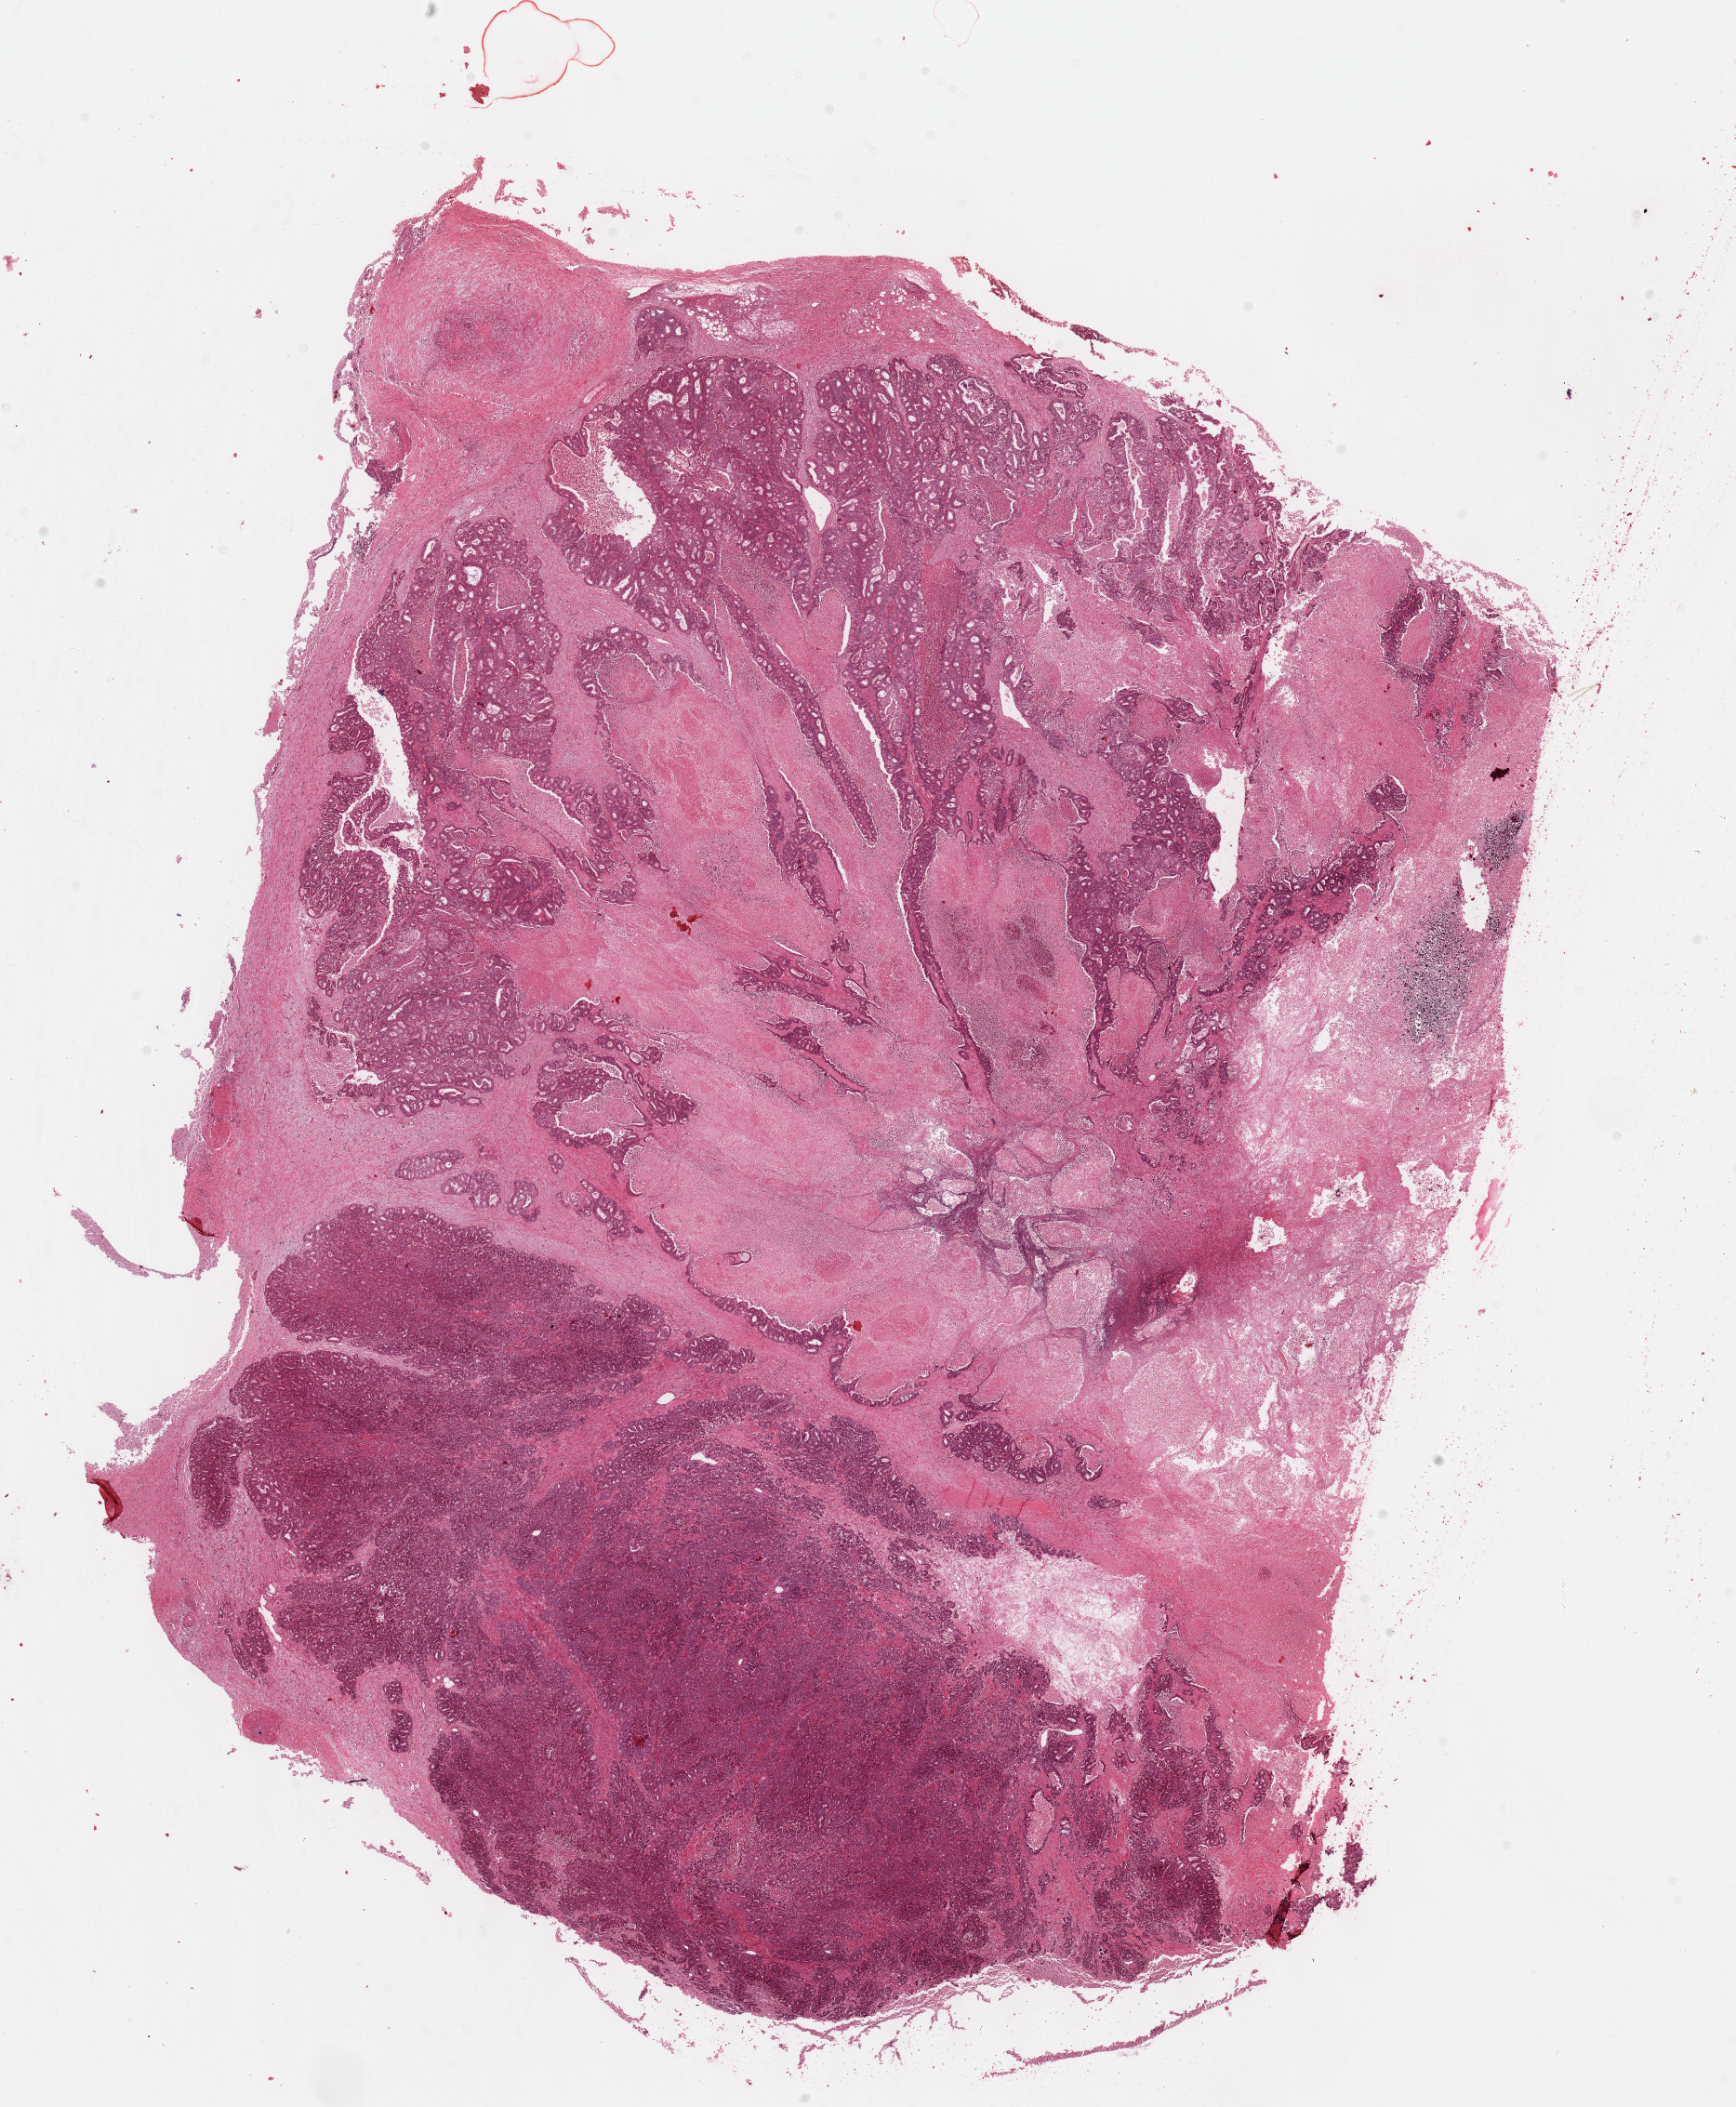
Whole-slide histology image, H&E-stained, a low-resolution overview of the entire scanned area, about 15.1 x 18.3 mm (from a 40x scan); formalin-fixed paraffin-embedded (FFPE) diagnostic section; stomach, primary tumour sample. Male, age 59 years at initial diagnosis. Histologic grade: G3 (poorly differentiated).
Lymph nodes positive (case pathology): 5 of 5 examined. AJCC pathologic stage: IIIA (6th edition). TNM: T3 N1 M0. Histologic diagnosis: Adenocarcinoma, NOS.